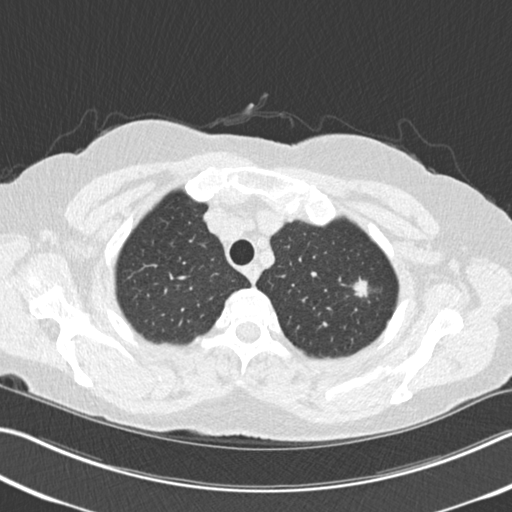
Axial slice from a low-dose chest CT screening exam; second annual screen; lung window (W 1500 / L -600 HU); slice 34 of 225 in the series; 512 × 512 image matrix. Female participant, aged 64 years at enrolment. Former smoker at enrolment.
Expert reader's lesion annotation, bounding box [x1, y1, x2, y2] px = [345, 271, 379, 304]. Screening reader's record for this exam (one nodule recorded; not confirmed to be the boxed lesion): non-calcified nodule or mass ≥4 mm, left upper lobe, 13 × 10 mm, spiculated (stellate) margins, soft tissue attenuation, pre-existing on the prior screen: yes; interval growth: yes.